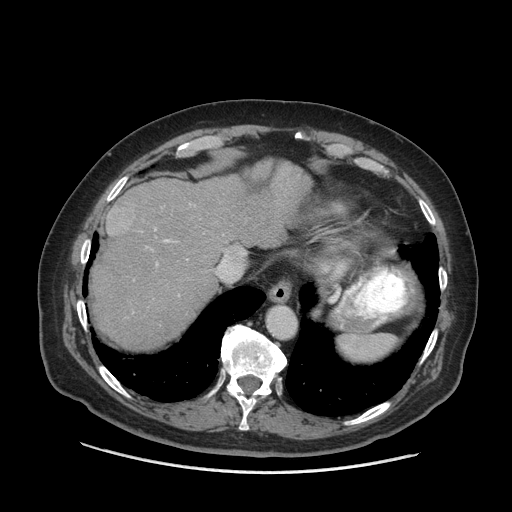
Contrast-enhanced abdominal CT (liver protocol), one axial slice. Position 57 of 77 along the scan axis. Reconstruction kernel STANDARD. 140 kVp. Soft-tissue window (W 400 / L 40 HU). 2.5 mm slice thickness. 512 × 512 image matrix, field of view 420 × 420 mm. From the clinical record (not read from this slice): diagnosis: hepatocellular carcinoma (patient treated with transarterial chemoembolisation; whether this scan precedes or follows treatment is not stated here); TNM stage (as recorded): Stage-I.
Structures marked on this image (semi-automatic segmentation, software-assisted and operator-edited):
- abdominal aorta: bounding box (x1, y1, x2, y2) in pixels: (268, 306, 296, 337)
- liver parenchyma outside the tumour (the mass and vessels are separate outlines, so this box may not span the whole liver): (90, 162, 310, 350)
- mass: (106, 205, 134, 237)
- liver vessels: (155, 229, 170, 242)